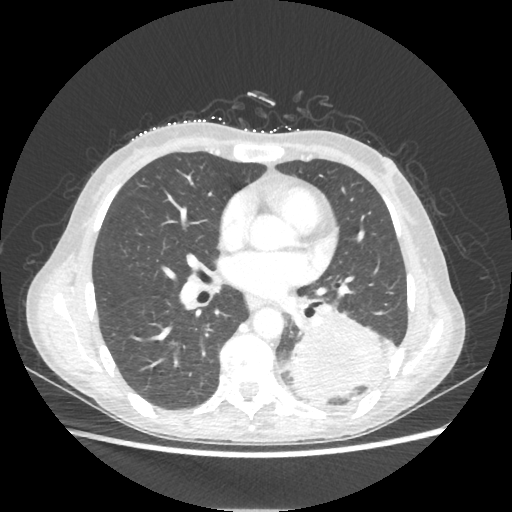
Chest CT, one axial slice; slice 107 of 221 in the series (ordered by position); 80 kVp; lung window (W 1500 / L -600 HU); 1.25 mm slice thickness; 512 × 512 image matrix. Female patient, age 53 years. From the clinical record (not read from this slice): clinical TNM (as recorded): T3 N0 M0.
Annotated regions visible in this slice (rectangle marked by the reading radiologist):
- lung tumour (recorded histology: adenocarcinoma): bounding box <287,311,385,402> (left, top, right, bottom; pixels)